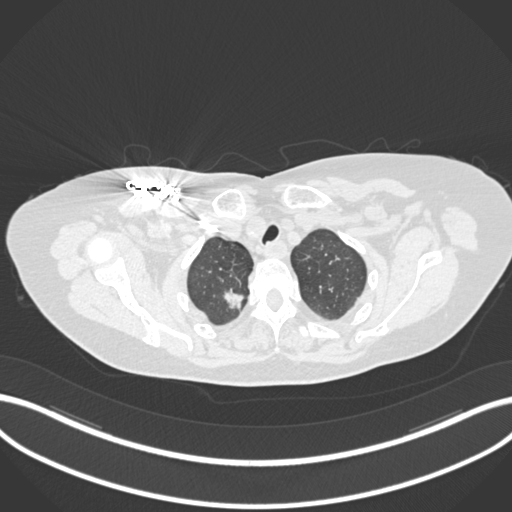
Chest CT, one axial slice. Position 157 of 176 along the scan axis. Reconstruction kernel B30f. Lung window (W 1500 / L -600 HU). 1 mm slice thickness. 512 × 512 image matrix. Patient: female, 72 years. Case-level facts recorded for this patient, not image findings: clinical TNM (as recorded): T1c N0 M0.
Annotated regions visible in this slice (rectangle marked by the reading radiologist):
- lung tumour (recorded histology: adenocarcinoma): bounding box [x1, y1, x2, y2] px = [217, 286, 248, 316]